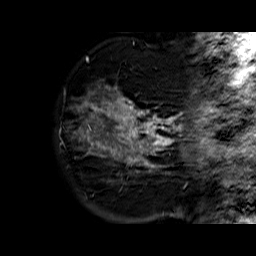
Breast MRI (dynamic contrast-enhanced), one sagittal slice. Dynamic contrast-enhanced series, time point 2 of 6 at this slice position (early post-contrast). 1.5 T. TE 6.3 ms, TR 32.4 ms. 256 × 256 image matrix. Female patient. From the clinical record (not read from this slice): setting: breast cancer imaged before/during neoadjuvant chemotherapy; receptor status: HR-positive, HER2-negative.
Structures marked on this image (semi-automatic segmentation, software-assisted and operator-edited):
- analysis volume of interest (the breast-tissue region the enhancement analysis was run in; not a lesion): box from (x=71, y=83) to (x=177, y=183) px
- tumour enhancement mask (voxels above the 100 % enhancement threshold inside the analysis volume of interest): (x=79, y=86)–(x=177, y=173)